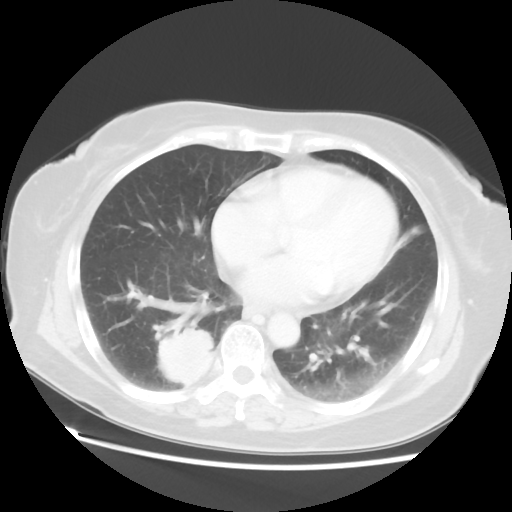
Chest CT, one axial slice. Slice 23 of 52 in the series (ordered by position). 120 kVp. Lung window (W 1500 / L -600 HU). 5 mm slice thickness. 512 × 512 image matrix. Female patient, age 69 years. From the clinical record (not read from this slice): clinical TNM (as recorded): T2 N1 M1a.
Annotated regions visible in this slice (rectangle marked by the reading radiologist):
- lung tumour (recorded histology: adenocarcinoma): box from (x=157, y=324) to (x=217, y=393) px